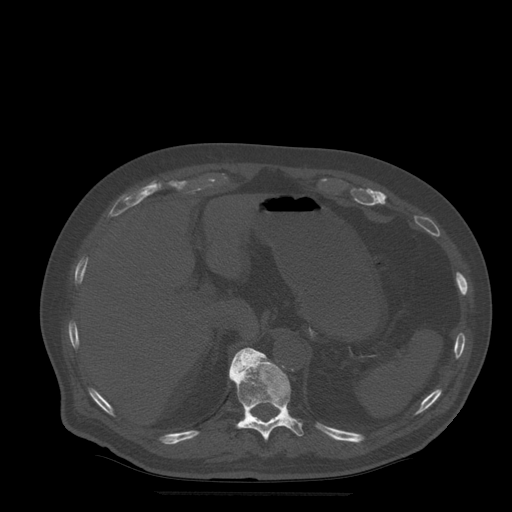
CT including the spine, one axial slice. Slice 243 of 522 in the series (ordered by position). Bone window (W 1800 / L 400 HU). 1.25 mm slice thickness. 512 × 512 image matrix, field of view 420 × 420 mm. Patient age 72 years. Case-level facts recorded for this patient, not image findings: primary cancer: prostate.
Annotated regions visible in this slice (semi-automatic segmentation, software-assisted and operator-edited):
- T11 vertebra: bounding box <229,348,304,441> (left, top, right, bottom; pixels)
- T12 vertebra: <231,352,240,366>